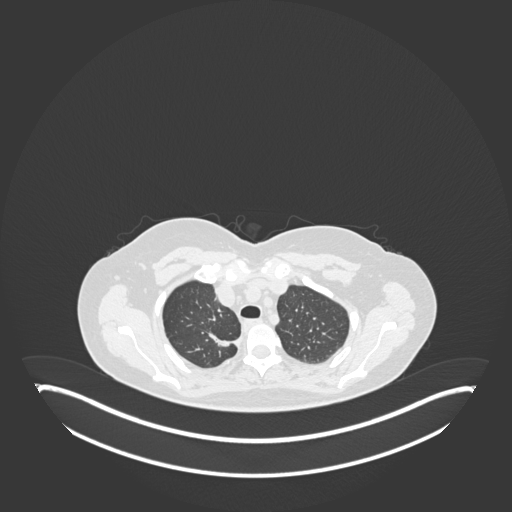
Chest CT, one axial slice; position 146 of 181 along the scan axis; reconstruction kernel B30f; lung window (W 1500 / L -600 HU); 512 × 512 image matrix, field of view 500 × 500 mm. Female patient, age 65 years. From the clinical record (not read from this slice): clinical TNM (as recorded): T1b N0 M0; histopathological grade: G2.
Structures marked on this image (rectangle marked by the reading radiologist):
- lung tumour (recorded histology: adenocarcinoma): bounding box [x1, y1, x2, y2] px = [204, 328, 241, 353]